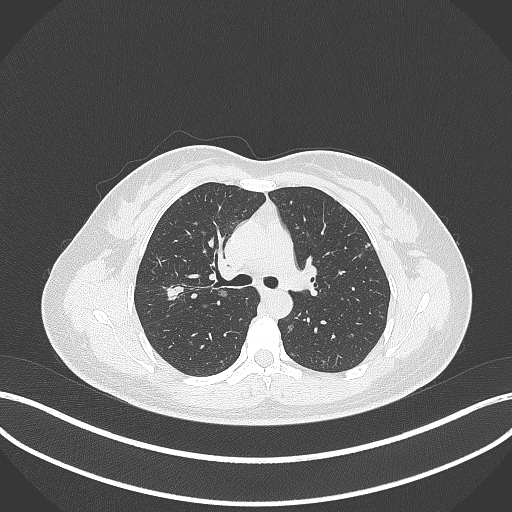
Chest CT, one axial slice; position 218 of 307 along the scan axis; 120 kVp; lung window (W 1500 / L -600 HU); 1 mm slice thickness; 512 × 512 image matrix. Patient: female, 33 years. From the clinical record (not read from this slice): clinical TNM (as recorded): T1c N0 M0.
Annotated regions visible in this slice (rectangle marked by the reading radiologist):
- lung tumour (recorded histology: adenocarcinoma): bounding box (x1, y1, x2, y2) in pixels: (165, 282, 184, 303)